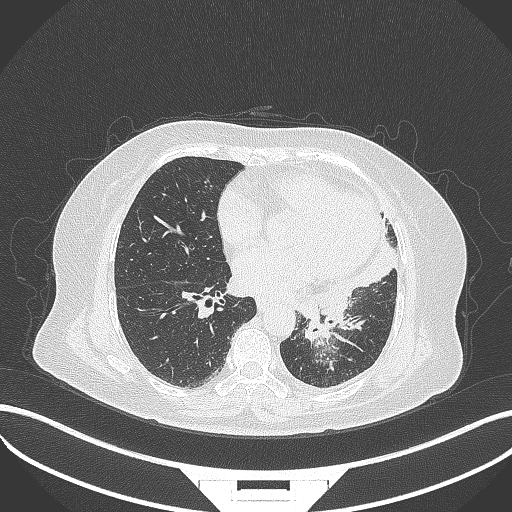
Chest CT, one axial slice; position 147 of 322 along the scan axis; reconstruction kernel B70f; lung window (W 1500 / L -600 HU); 1 mm slice thickness; 512 × 512 image matrix, field of view 400 × 400 mm. Female patient, age 69 years. From the clinical record (not read from this slice): clinical TNM (as recorded): T2b N3 M1.
Annotated regions visible in this slice (bounding box drawn by a radiologist):
- lung tumour (recorded histology: adenocarcinoma): bounding box [x1, y1, x2, y2] px = [301, 311, 331, 346]